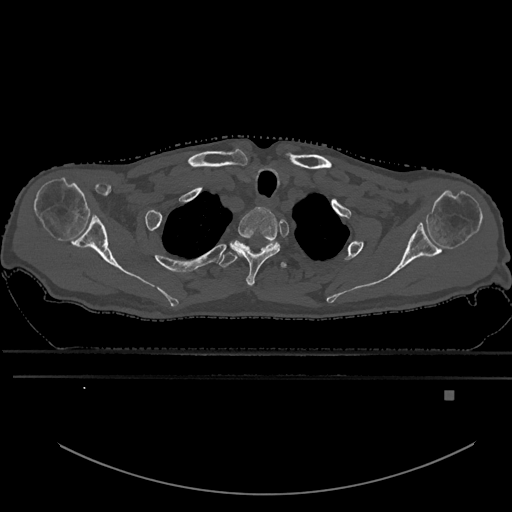
CT including the spine, one axial slice; slice 524 of 969 in the series (ordered by position); bone window (W 1800 / L 400 HU); 0.5 mm slice thickness; 512 × 512 image matrix, field of view 456 × 456 mm. Patient: male, 82 years. Case-level facts recorded for this patient, not image findings: primary cancer: prostate; vertebrae with lytic lesions (as recorded): T11, T9, T8, T2.
Annotated regions visible in this slice (semi-automatic segmentation, software-assisted and operator-edited):
- T1 vertebra: bounding box <231,207,281,287> (left, top, right, bottom; pixels)
- T2 vertebra: <219,238,280,267>